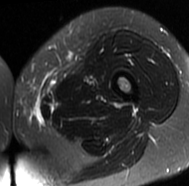
MRI of an extremity soft-tissue mass, one axial slice; position 16 of 77 along the scan axis; T2-weighted fat-saturated; MR volume resampled by the dataset authors to the PET/CT grid (not the native acquisition matrix); 3.27 mm slice thickness; 189 × 186 image matrix, field of view 185 × 182 mm. Female patient. Case-level facts recorded for this patient, not image findings: histological type: leiomyosarcoma; grade: high; site of the primary tumour: groin.
Annotated regions visible in this slice (expert contour drawn on MRI and transferred to this co-registered scan by the dataset authors):
- gross tumour volume including surrounding oedema: bounding box [x1, y1, x2, y2] px = [15, 101, 43, 123]